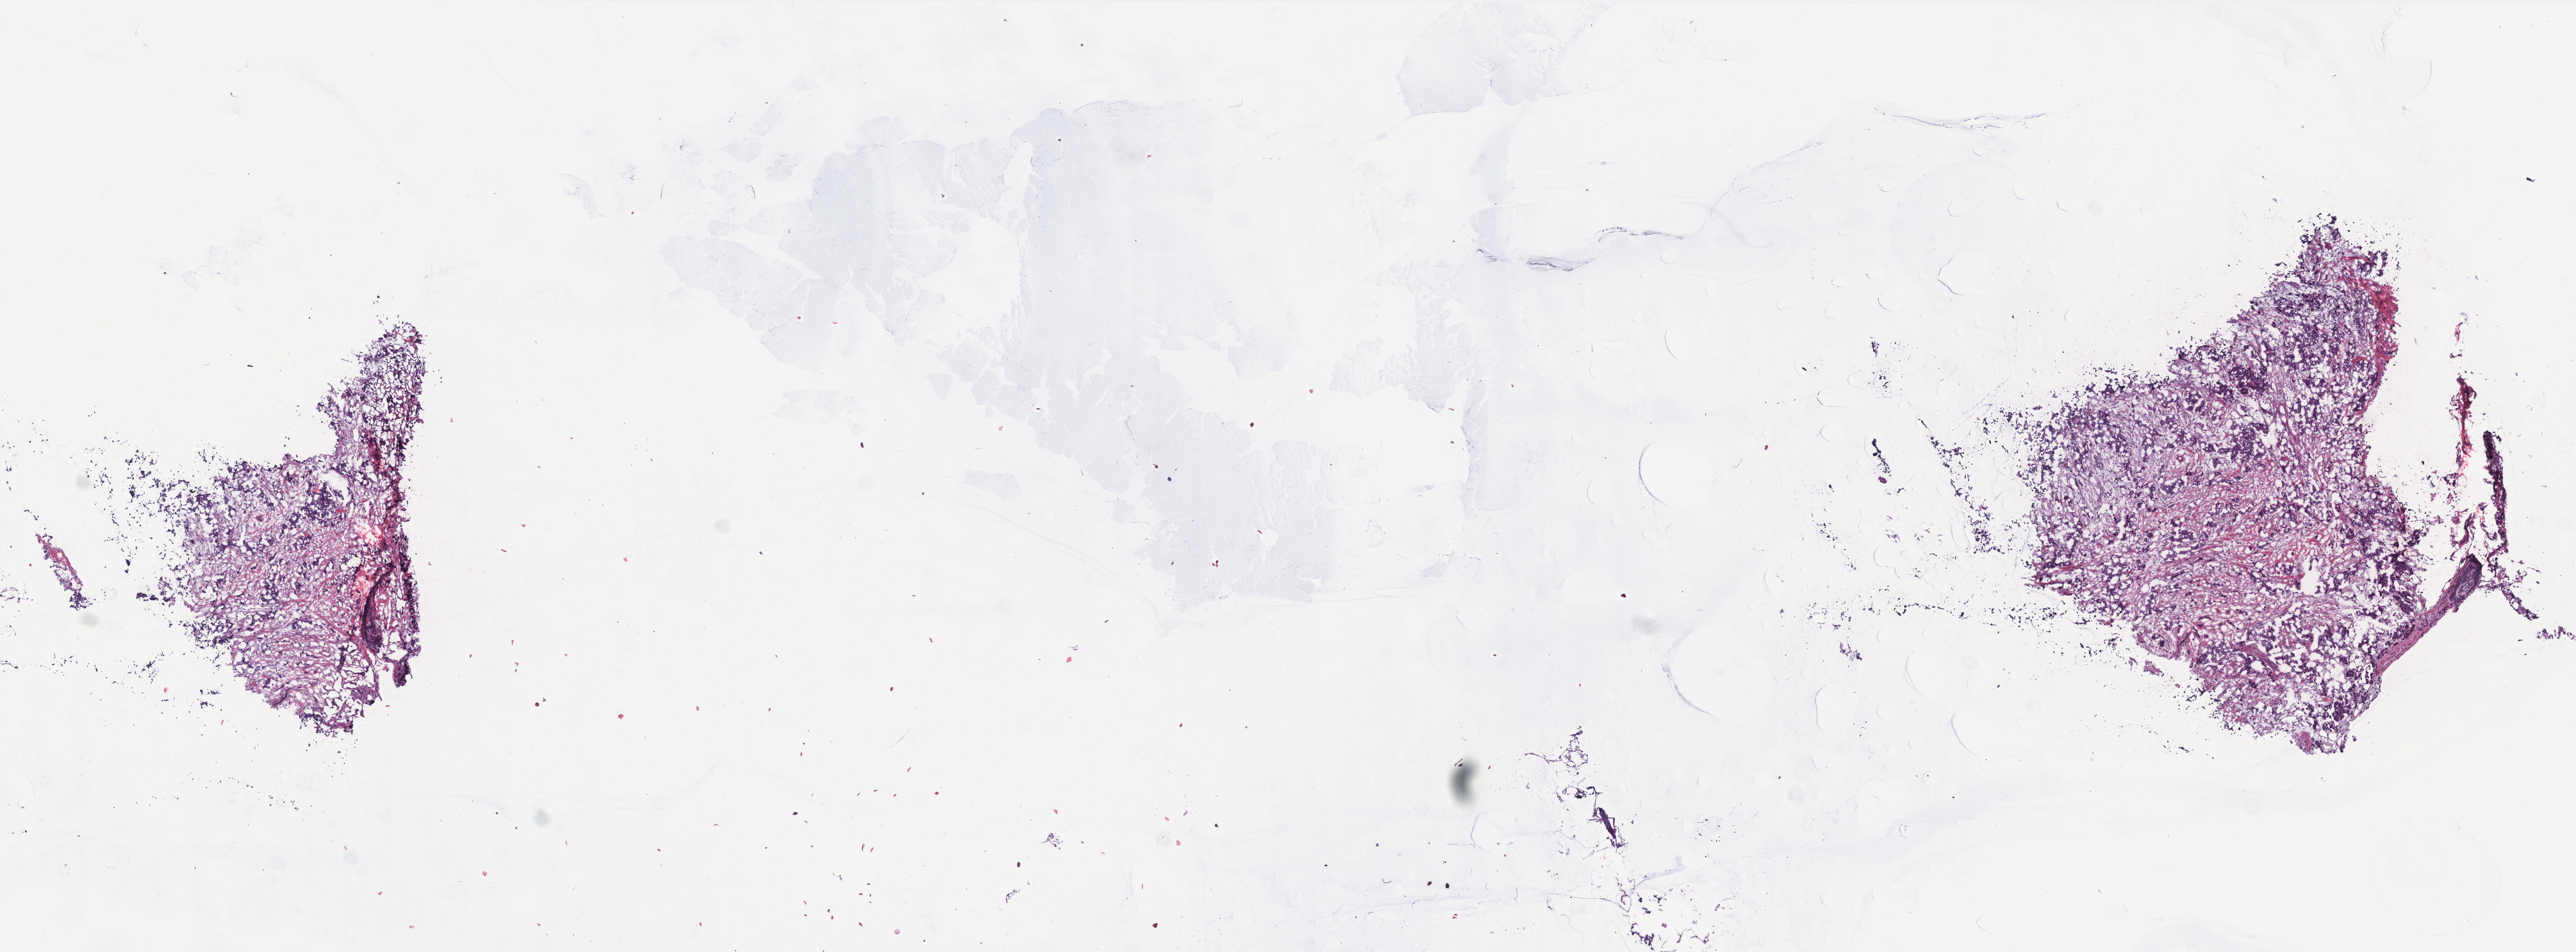
Digitized H&E tissue section (whole slide) — a low-resolution overview of the entire scanned area, about 16.1 x 6.0 mm. Frozen section. Breast, primary tumour sample. Patient: female, age at initial diagnosis 41 years. Pathologist review of this section (percent, as recorded): tumour cells 35%, tumour nuclei 70%, normal cells 55%, stromal cells 9%, necrosis 1%. Inflammatory infiltration, as recorded: lymphocyte infiltration 5%, monocyte infiltration 0%, neutrophil infiltration 0%.
Pathologic diagnosis: Infiltrating duct carcinoma, NOS. Lymph nodes positive (case pathology): 0 of 2 examined. AJCC pathologic stage: I (6th edition).